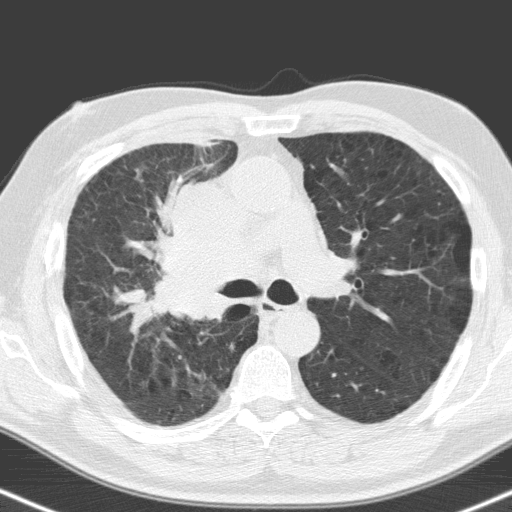
Low-dose screening chest CT, one axial slice. Position 105 of 160 along the scan axis. 120 kVp. Lung window (W 1500 / L -600 HU). 3.2 mm slice thickness. 512 × 512 image matrix, field of view 324 × 324 mm.
Structures marked on this image (expert manual segmentation):
- lesion 1 (tumor, hilum of right lung): bounding box (x1, y1, x2, y2) in pixels: (156, 181, 262, 319)